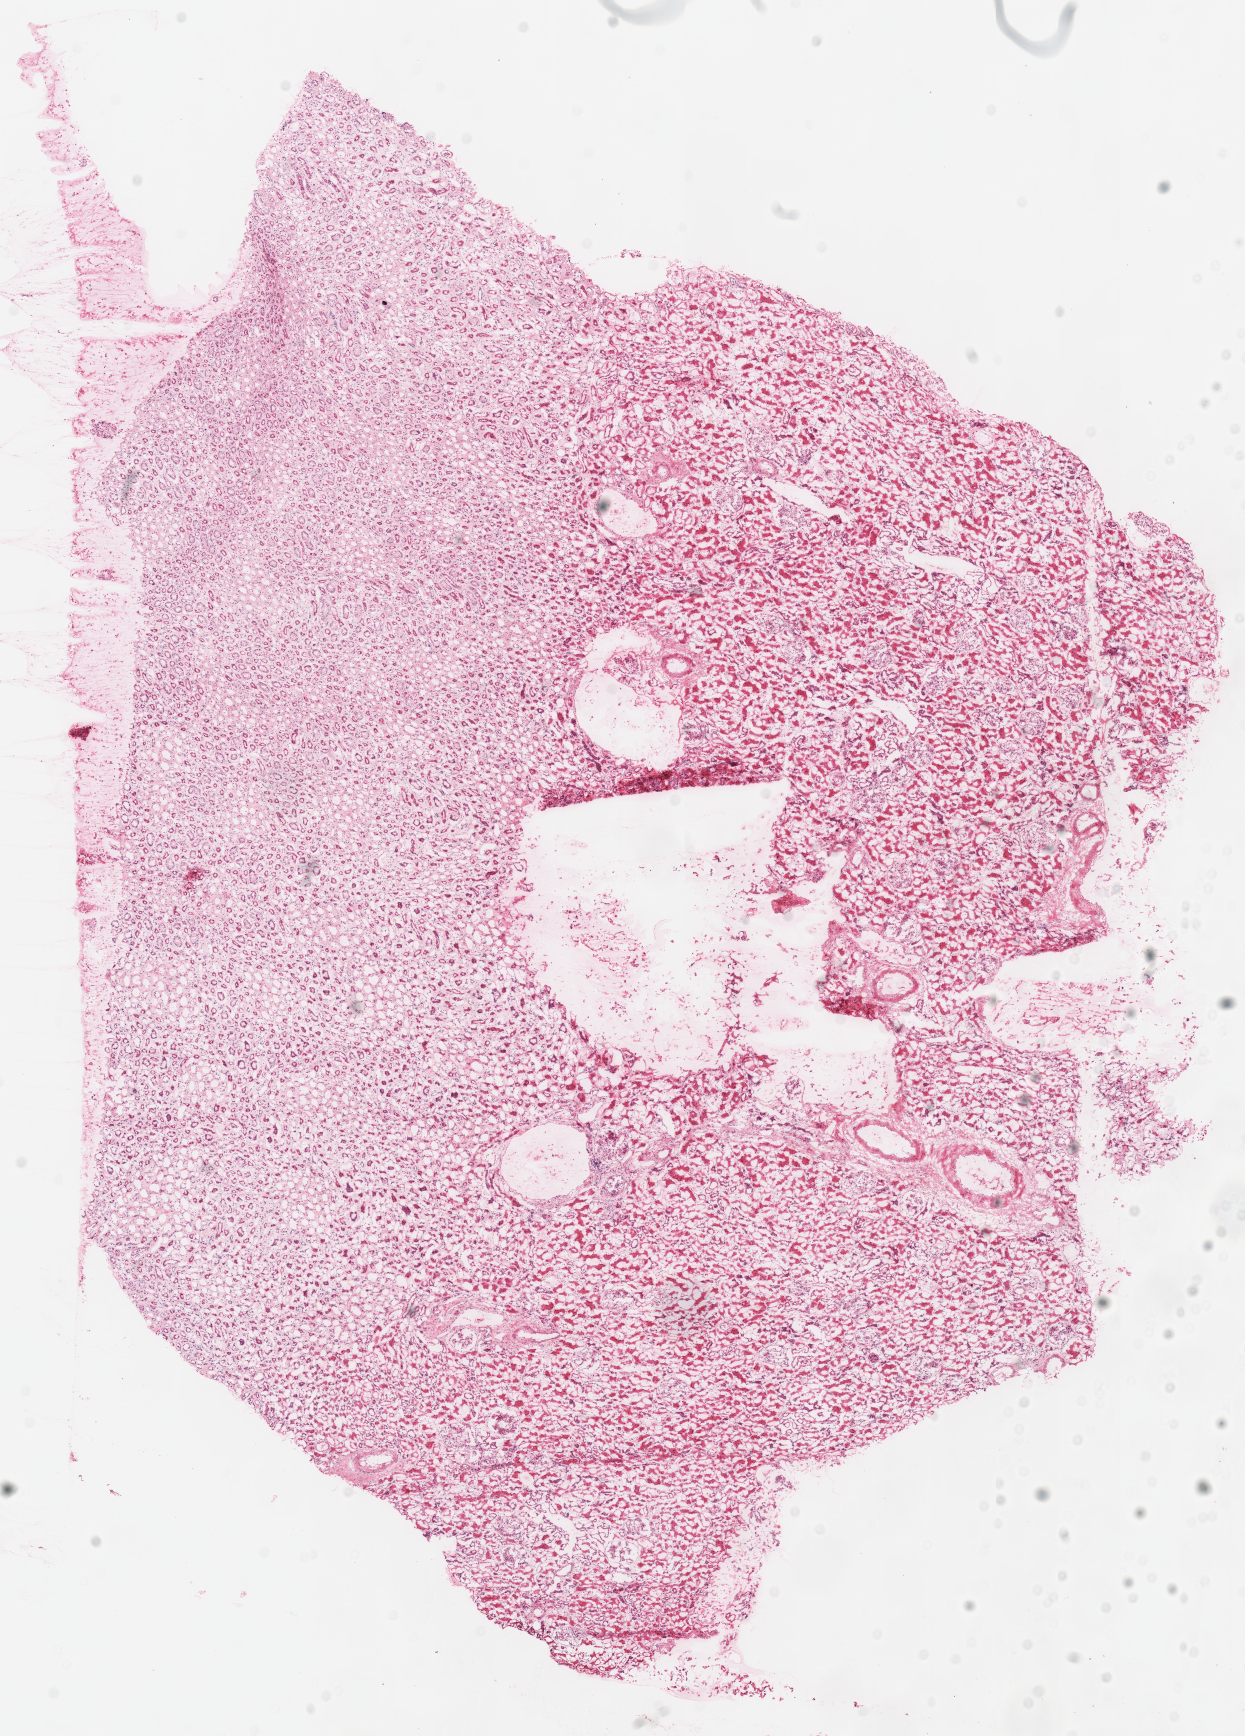
Whole-slide histology image, H&E, a low-resolution overview of the entire scanned area, about 9.8 x 13.6 mm, frozen section from the top of the tissue portion, solid tissue normal (non-tumour tissue) sample from the kidney. Female patient; age at initial diagnosis 41 years. Inflammatory infiltration, as recorded: lymphocyte infiltration 0%, monocyte infiltration 0%, neutrophil infiltration 0%.
- this section: solid tissue normal sample (biorepository sample class)
- patient diagnosis: Renal cell carcinoma, chromophobe type